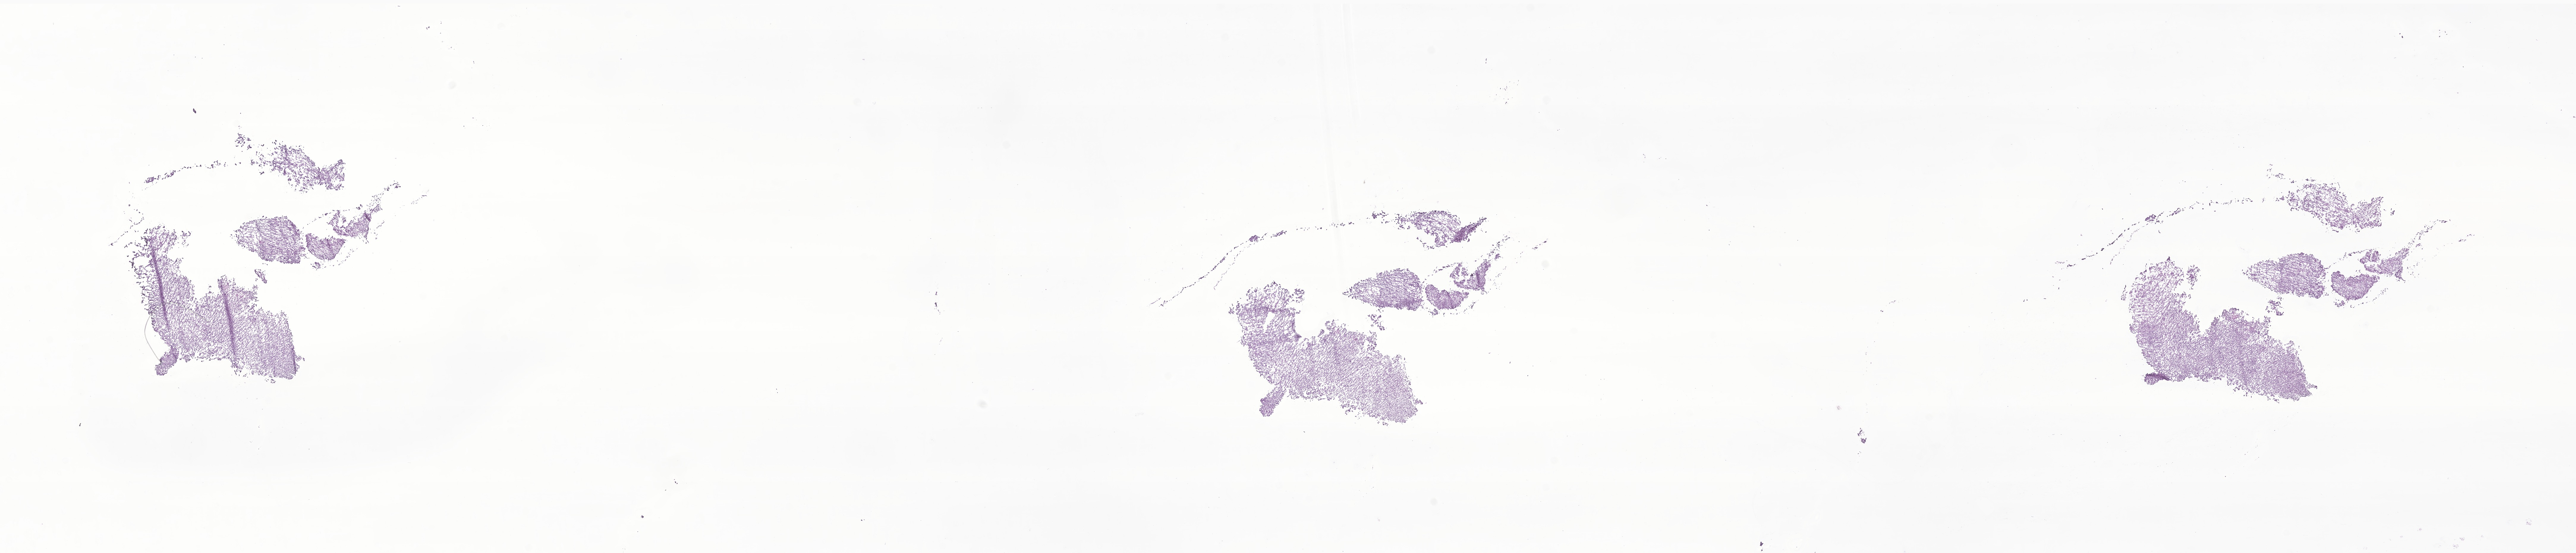
Whole-slide image, hematoxylin and eosin (H&E) stain of tumor tissue from the brain, low-resolution overview of the scanned area, about 36.5 x 7.8 mm, frozen section. Patient male; age 183 months (15 years 3 months).
• diagnosis: Atypical teratoid/rhabdoid tumor